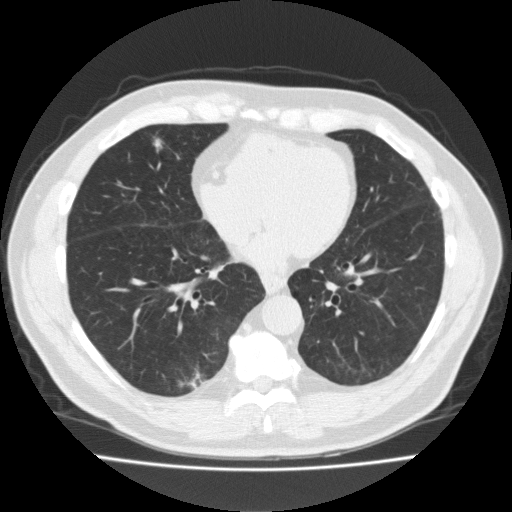
Low-dose screening chest CT, one axial slice; slice 70 of 184 in the series (ordered by position); reconstruction kernel FC10; 120 kVp; lung window (W 1500 / L -600 HU); 2 mm slice thickness; 512 × 512 image matrix, field of view 369 × 369 mm.
Annotated regions visible in this slice (manually delineated by an expert):
- lesion 1 (tumor, middle lobe of right lung): bounding box [x1, y1, x2, y2] px = [154, 139, 162, 152]